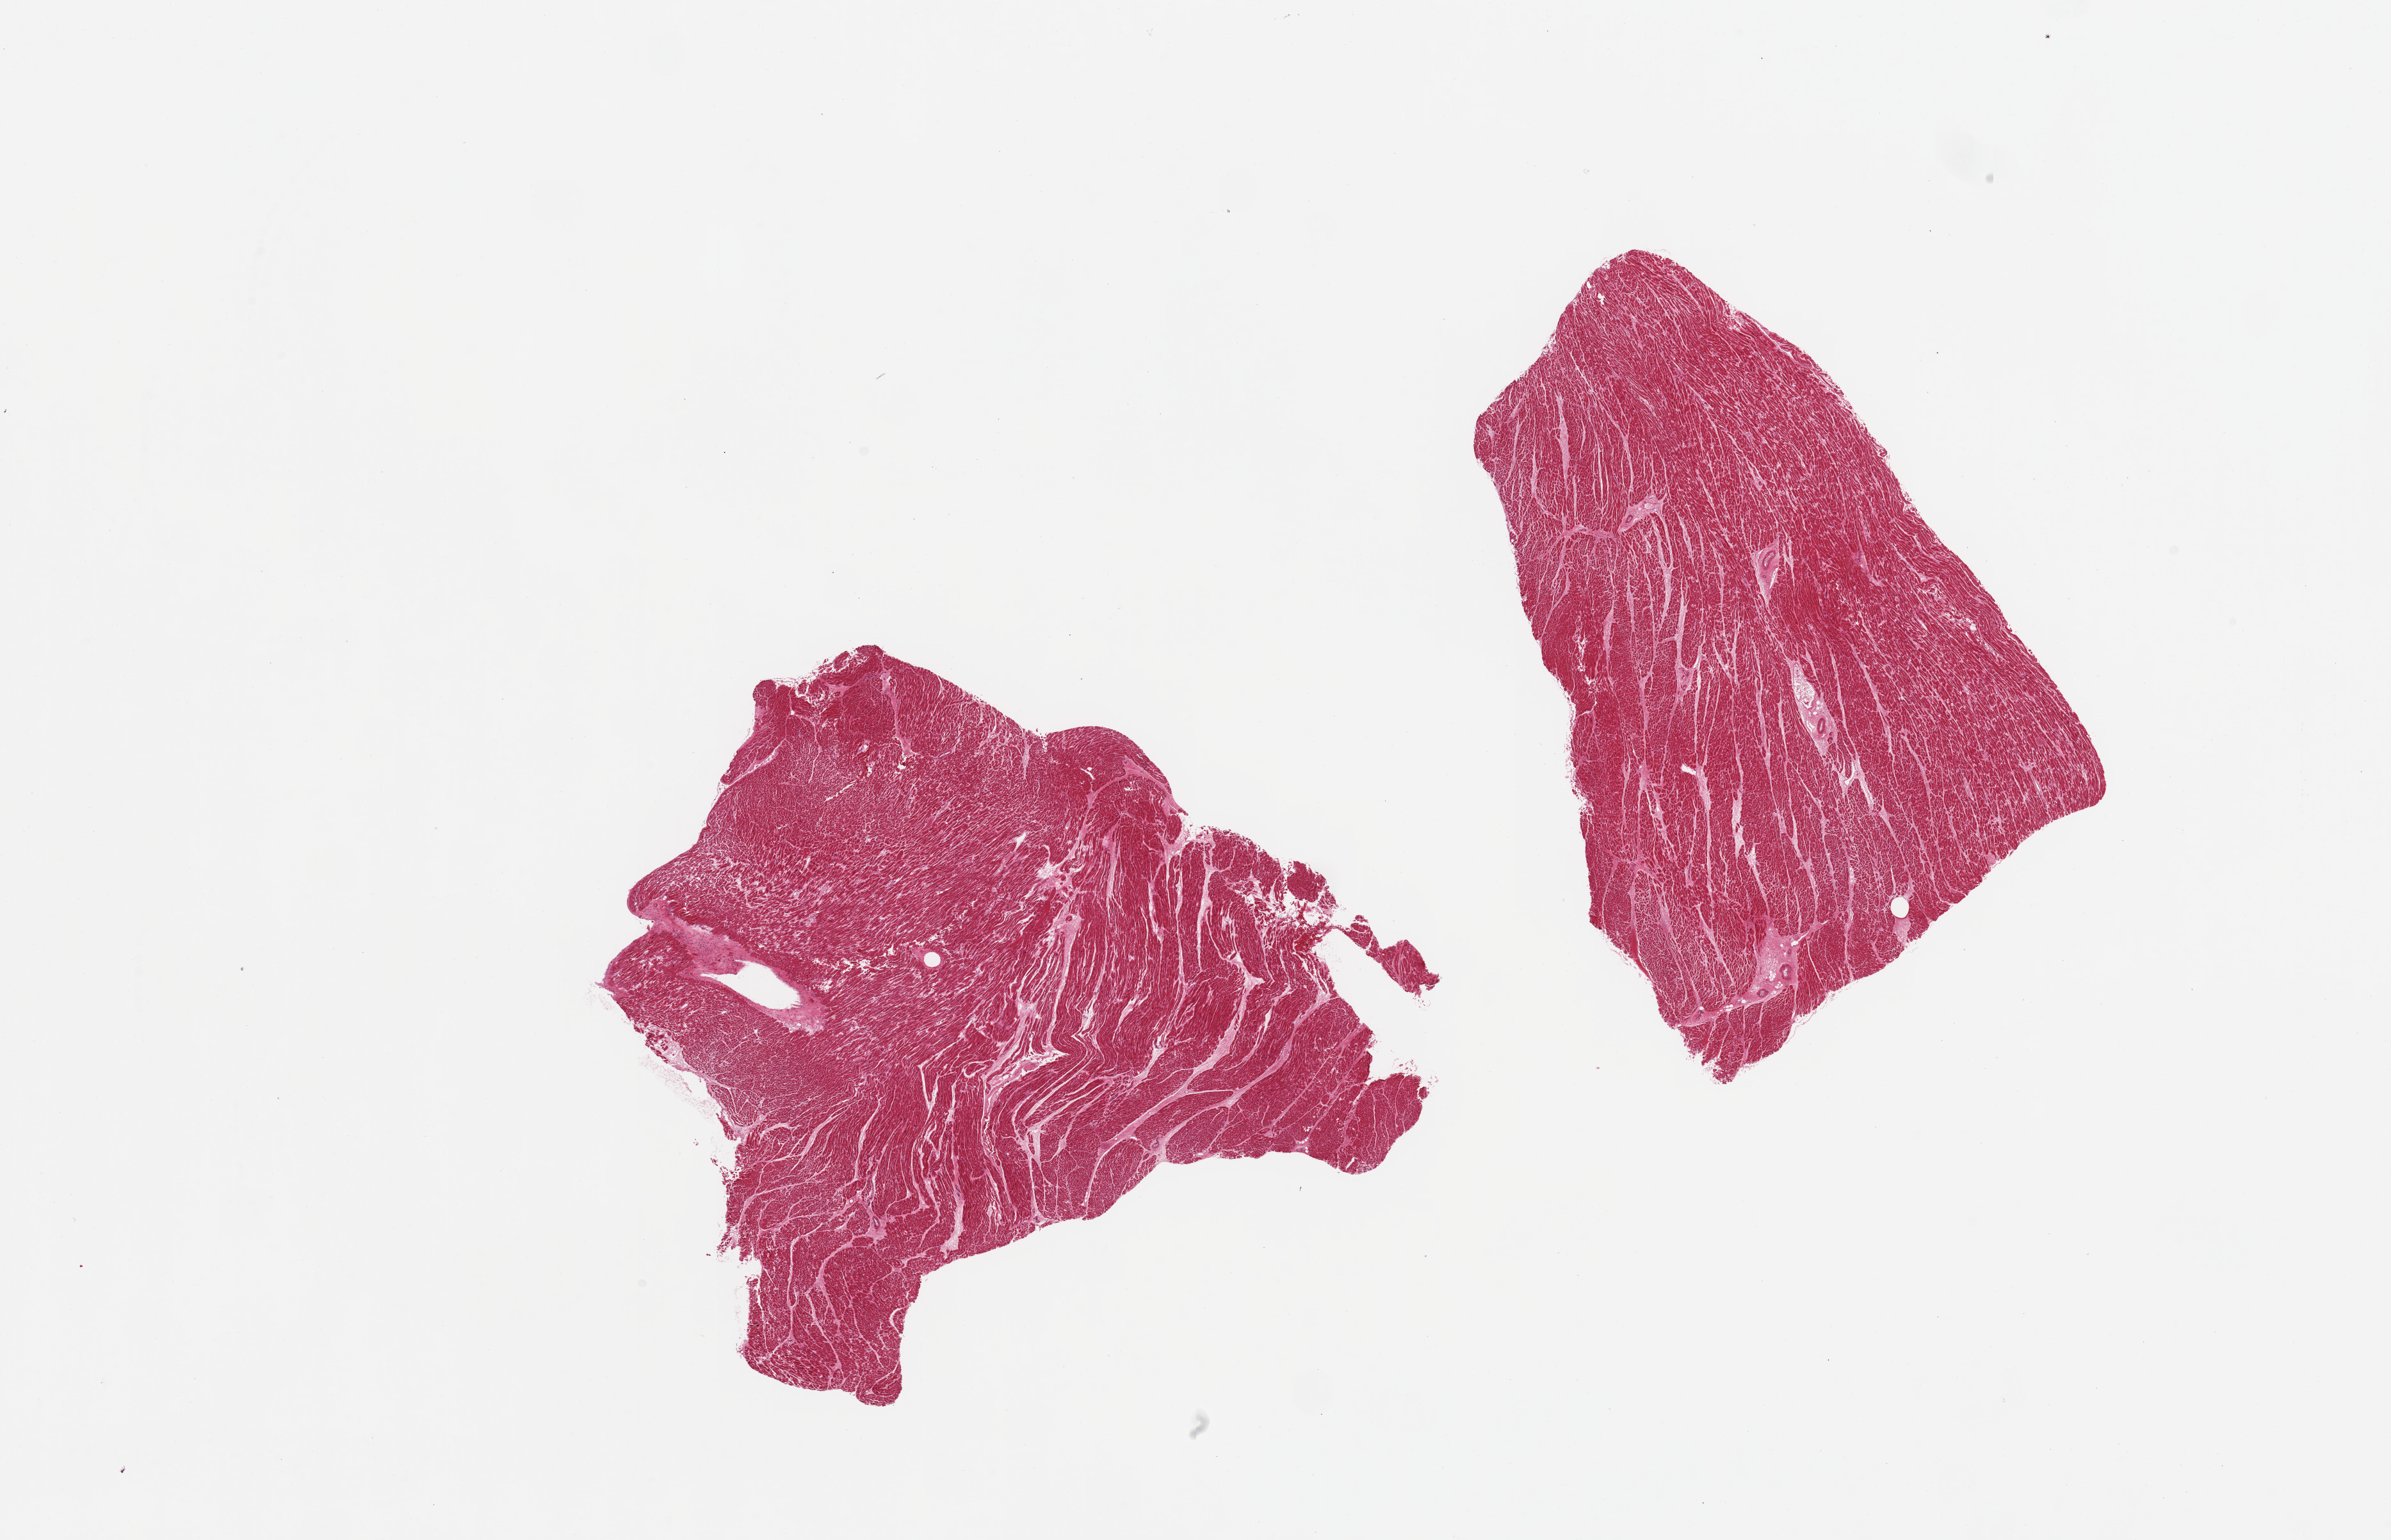
H&E whole-slide image, a low-resolution overview of the entire scanned area, about 29.5 x 19.0 mm (slide scanned at 20x), PAXgene-fixed paraffin-embedded (PFPE) section, target tissue: heart, tissue donor sample. Donor: male.
Pathologist's review note for this sample: 2 pieces, moderate interstitial fibrosis.